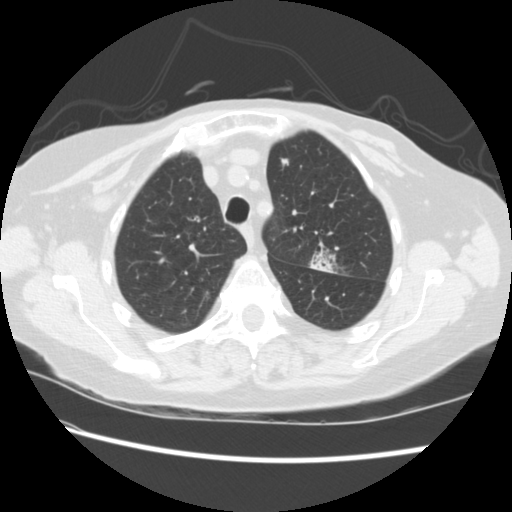
Low-dose screening chest CT, axial slice; baseline screening round; lung window (W 1500 / L -600 HU); 2.5 mm slice thickness; standard (soft-tissue) reconstruction kernel (STANDARD). Female, age 74 years at enrolment. Former smoker at enrolment.
Expert-annotated lung lesion, bounding box [x1, y1, x2, y2] px = [297, 237, 347, 280]. The screening reader recorded 2 non-calcified nodules or masses ≥4 mm on this exam (left upper lobe, right lower lobe); which of them this box marks is not recorded. Official screen result: positive, change unspecified: nodule(s) >= 4 mm or enlarging nodule(s), mass(es), or other non-specific abnormalities suspicious for lung cancer. Participant outcome: lung cancer diagnosed 309 days after this screen — non-small cell carcinoma, left upper lobe, stage IV (AJCC 6th edition).